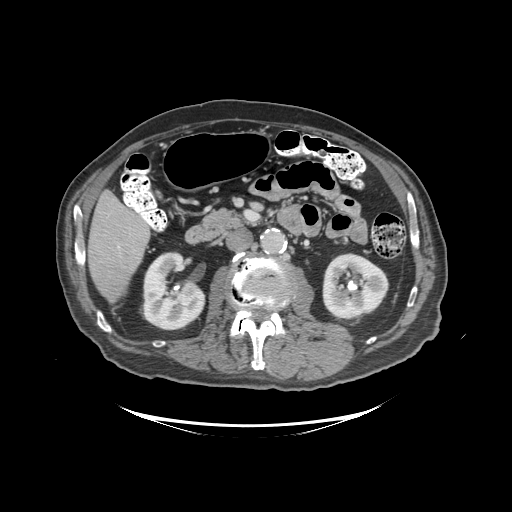
Contrast-enhanced abdominal CT (liver protocol), one axial slice. Position 38 of 99 along the scan axis. Reconstruction kernel STANDARD. Soft-tissue window (W 400 / L 40 HU). 2.5 mm slice thickness. 512 × 512 image matrix. Case-level facts recorded for this patient, not image findings: diagnosis: hepatocellular carcinoma (patient treated with transarterial chemoembolisation; whether this scan precedes or follows treatment is not stated here); TNM stage (as recorded): Stage-I; Child-Pugh class: A.
Structures marked on this image (semi-automatically segmented with operator editing):
- liver parenchyma outside the tumour (the mass and vessels are separate outlines, so this box may not span the whole liver): box from (x=88, y=190) to (x=149, y=303) px
- mass: (x=95, y=265)–(x=128, y=299)